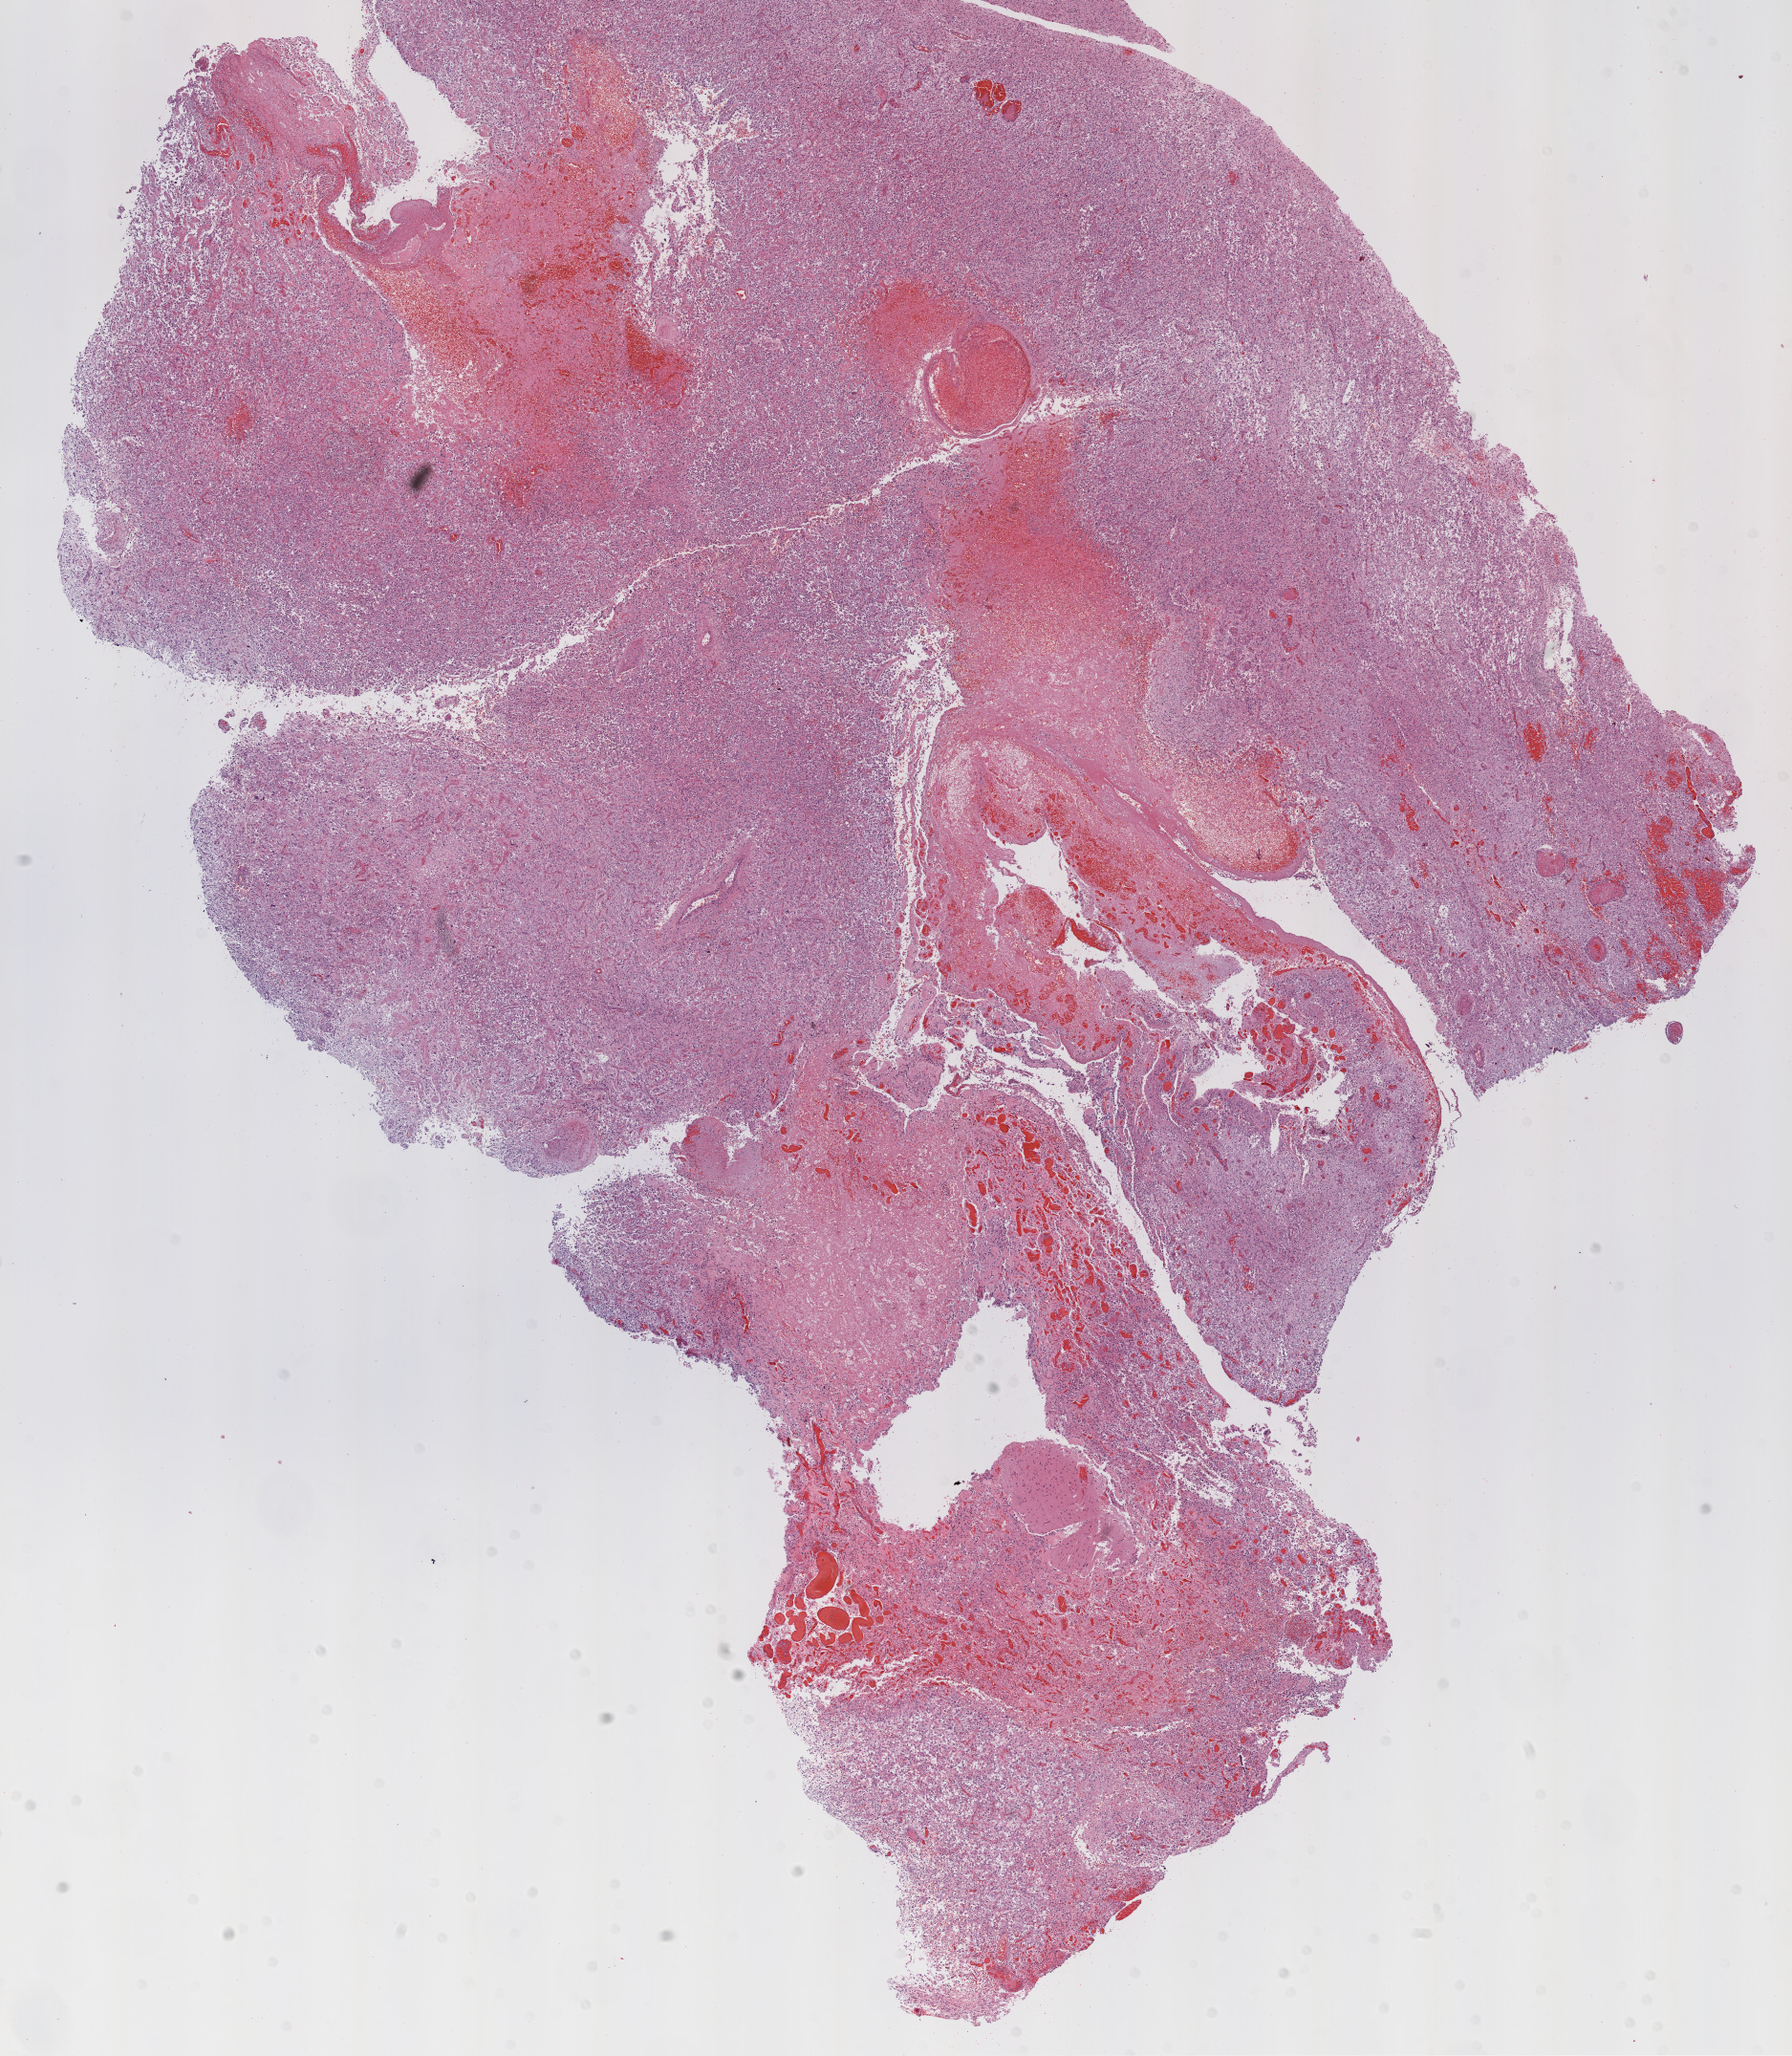
Whole-slide histology image, H&E-stained — a low-resolution overview of the entire scanned area, about 15.0 x 17.3 mm. Formalin-fixed paraffin-embedded (FFPE) diagnostic section. Sample: primary tumour, brain. Male patient; age at initial diagnosis 63 years.
Pathologic diagnosis: Glioblastoma.